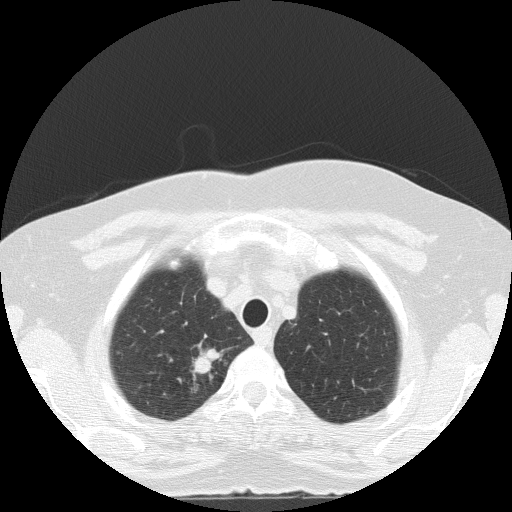
Axial slice from a low-dose chest CT screening exam; first (baseline) screen; lung window (W 1500 / L -600 HU); 2 mm slice thickness; 120 kVp; slice 19 of 133 in the series. Female participant, aged 56 years at enrolment. Current smoker at enrolment.
Expert-annotated lung lesion, box from (x=173, y=343) to (x=230, y=389) px. The screening reader recorded 2 non-calcified nodules or masses ≥4 mm on this exam; which of them this box marks is not recorded. Later outcome: lung cancer diagnosed 24 days after this screen — adenocarcinoma, NOS, right upper lobe, poorly differentiated (G3), stage IA (AJCC 6th edition), 20 mm at pathology.